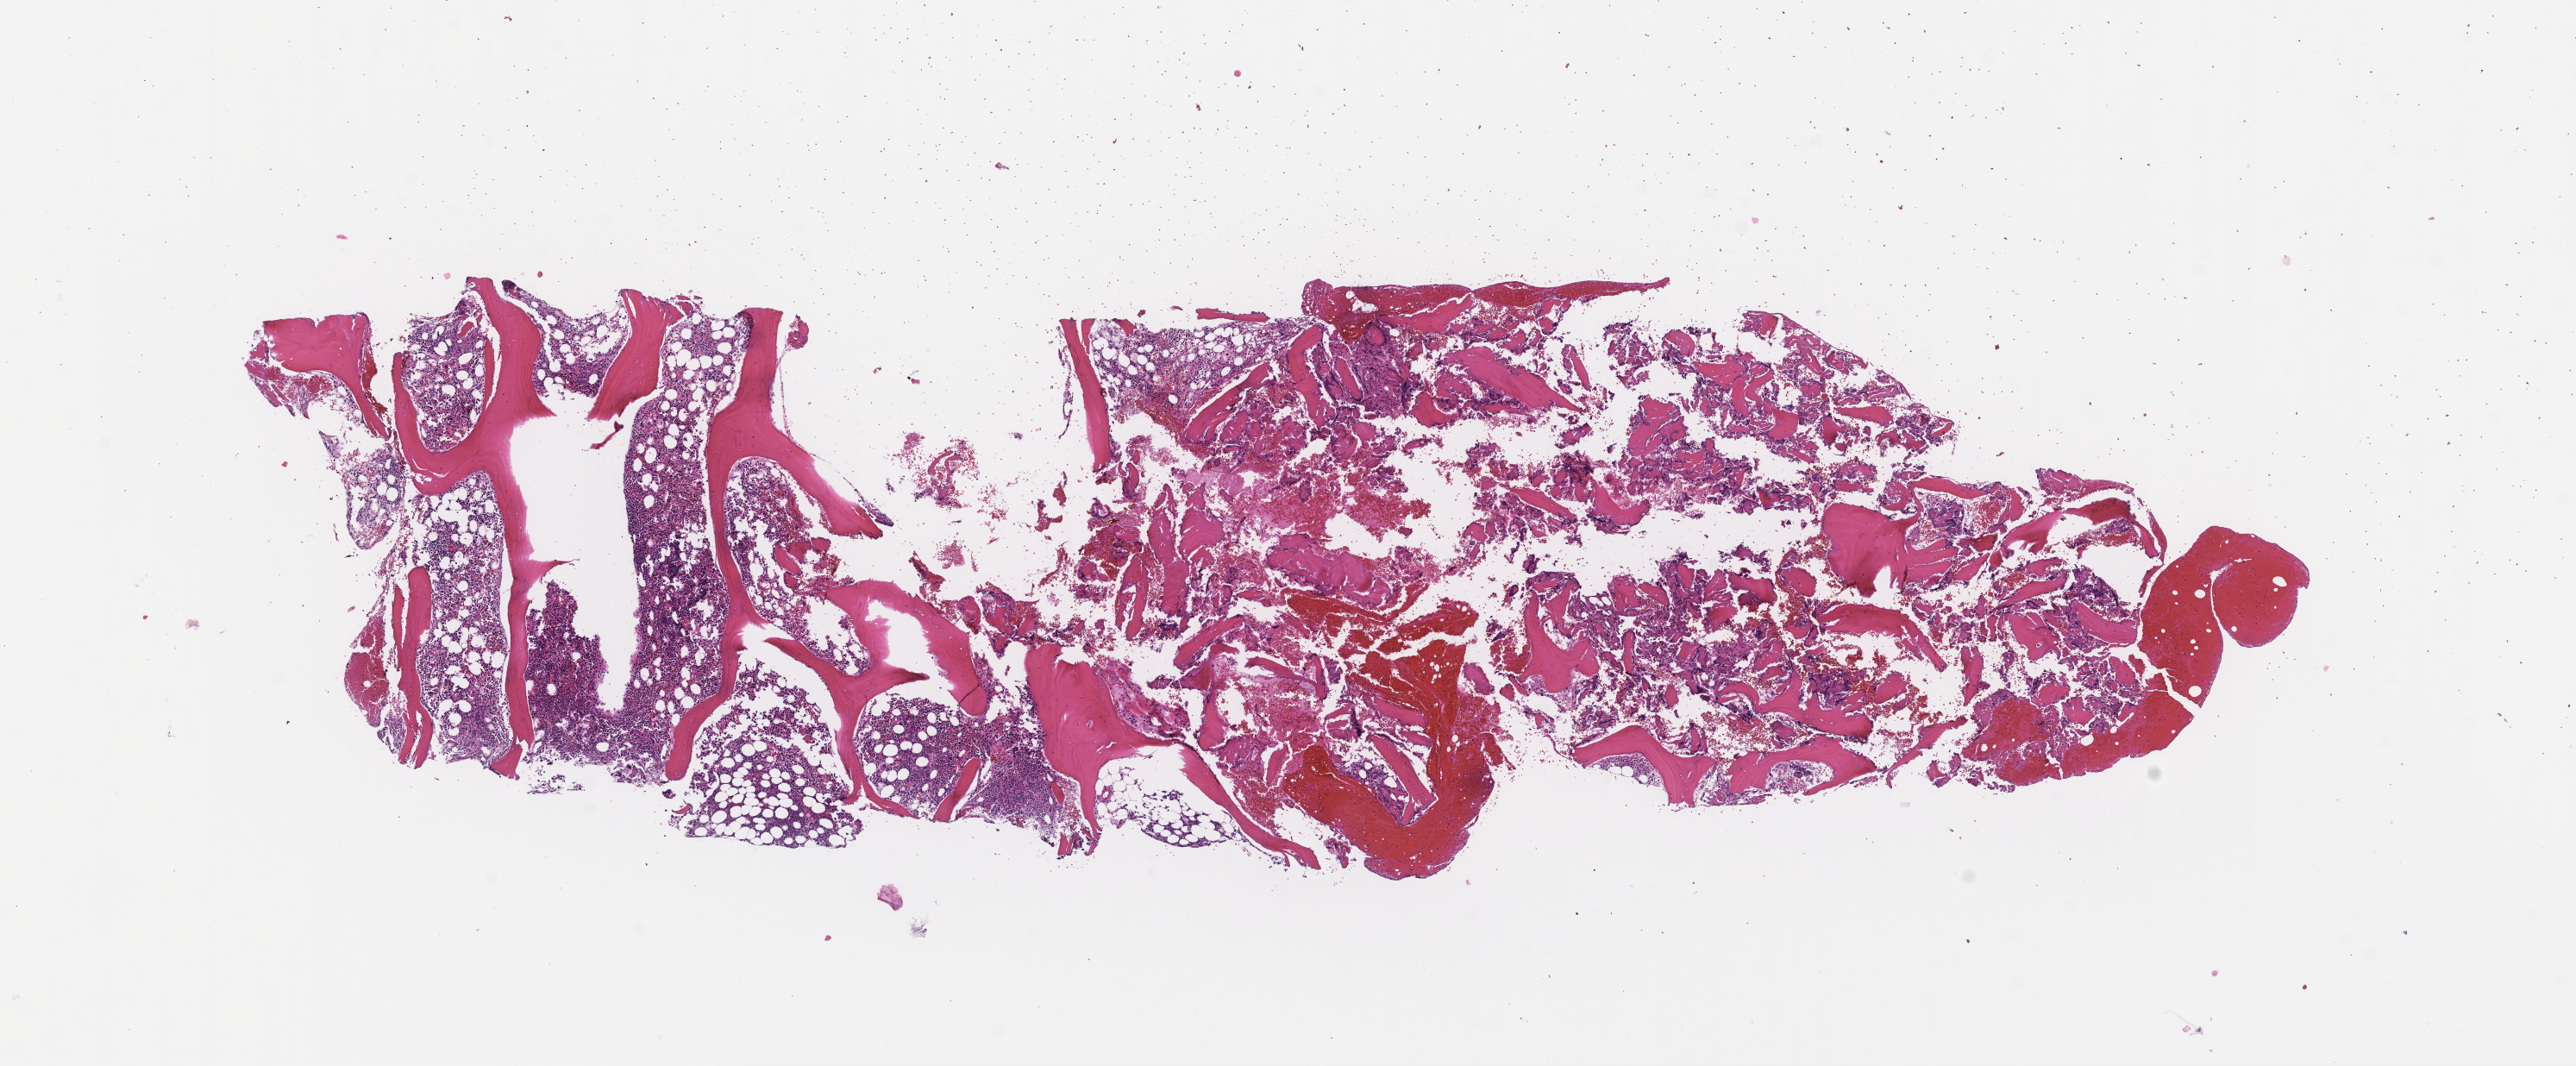
Whole-slide image, hematoxylin and eosin (H&E) stain — whole scanned area (about 12.1 x 5.0 mm) shown as a low-resolution overview; FFPE section; tissue site: bone marrow; specimen time point: collected at disease progression. Patient sex: female.
- this section: primary tumour tissue
- diagnosis: Acute Myeloid Leukemia Not Otherwise Specified